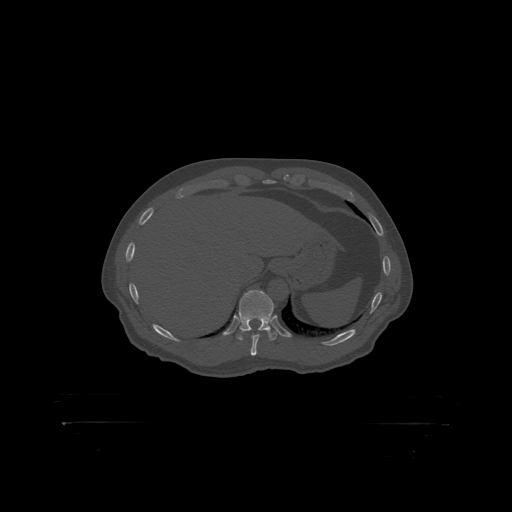
CT including the spine, one axial slice; position 388 of 399 along the scan axis; reconstruction kernel STANDARD; 120 kVp; bone window (W 1800 / L 400 HU); 512 × 512 image matrix, field of view 650 × 650 mm. Male patient, age 46 years. Case-level facts recorded for this patient, not image findings: primary cancer: skin.
Outlined on this slice (semi-automatic segmentation, software-assisted and operator-edited):
- T11 vertebra: bounding box <239,290,274,319> (left, top, right, bottom; pixels)